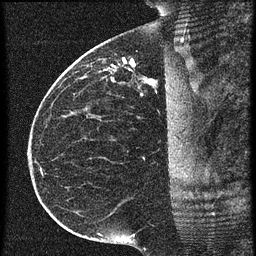
Breast MRI (dynamic contrast-enhanced), one sagittal slice. Slice 35 of 60 in the series (ordered by position). 3 images stored at this slice position (order not interpretable as contrast timing). 1.5 T. TE 4.2 ms, TR 20.4 ms. 1.5 mm slice thickness. 256 × 256 image matrix, field of view 200 × 200 mm. Female patient, age 35 years. From the clinical record (not read from this slice): setting: breast cancer imaged before/during neoadjuvant chemotherapy; receptor status: HR-positive, HER2-negative.
Outlined on this slice (semi-automatic segmentation, software-assisted and operator-edited):
- analysis volume of interest (the breast-tissue region the enhancement analysis was run in; not a lesion): bounding box <84,50,179,97> (left, top, right, bottom; pixels)
- tumour enhancement mask (voxels above the 90 % enhancement threshold inside the analysis volume of interest): <124,60,155,85>